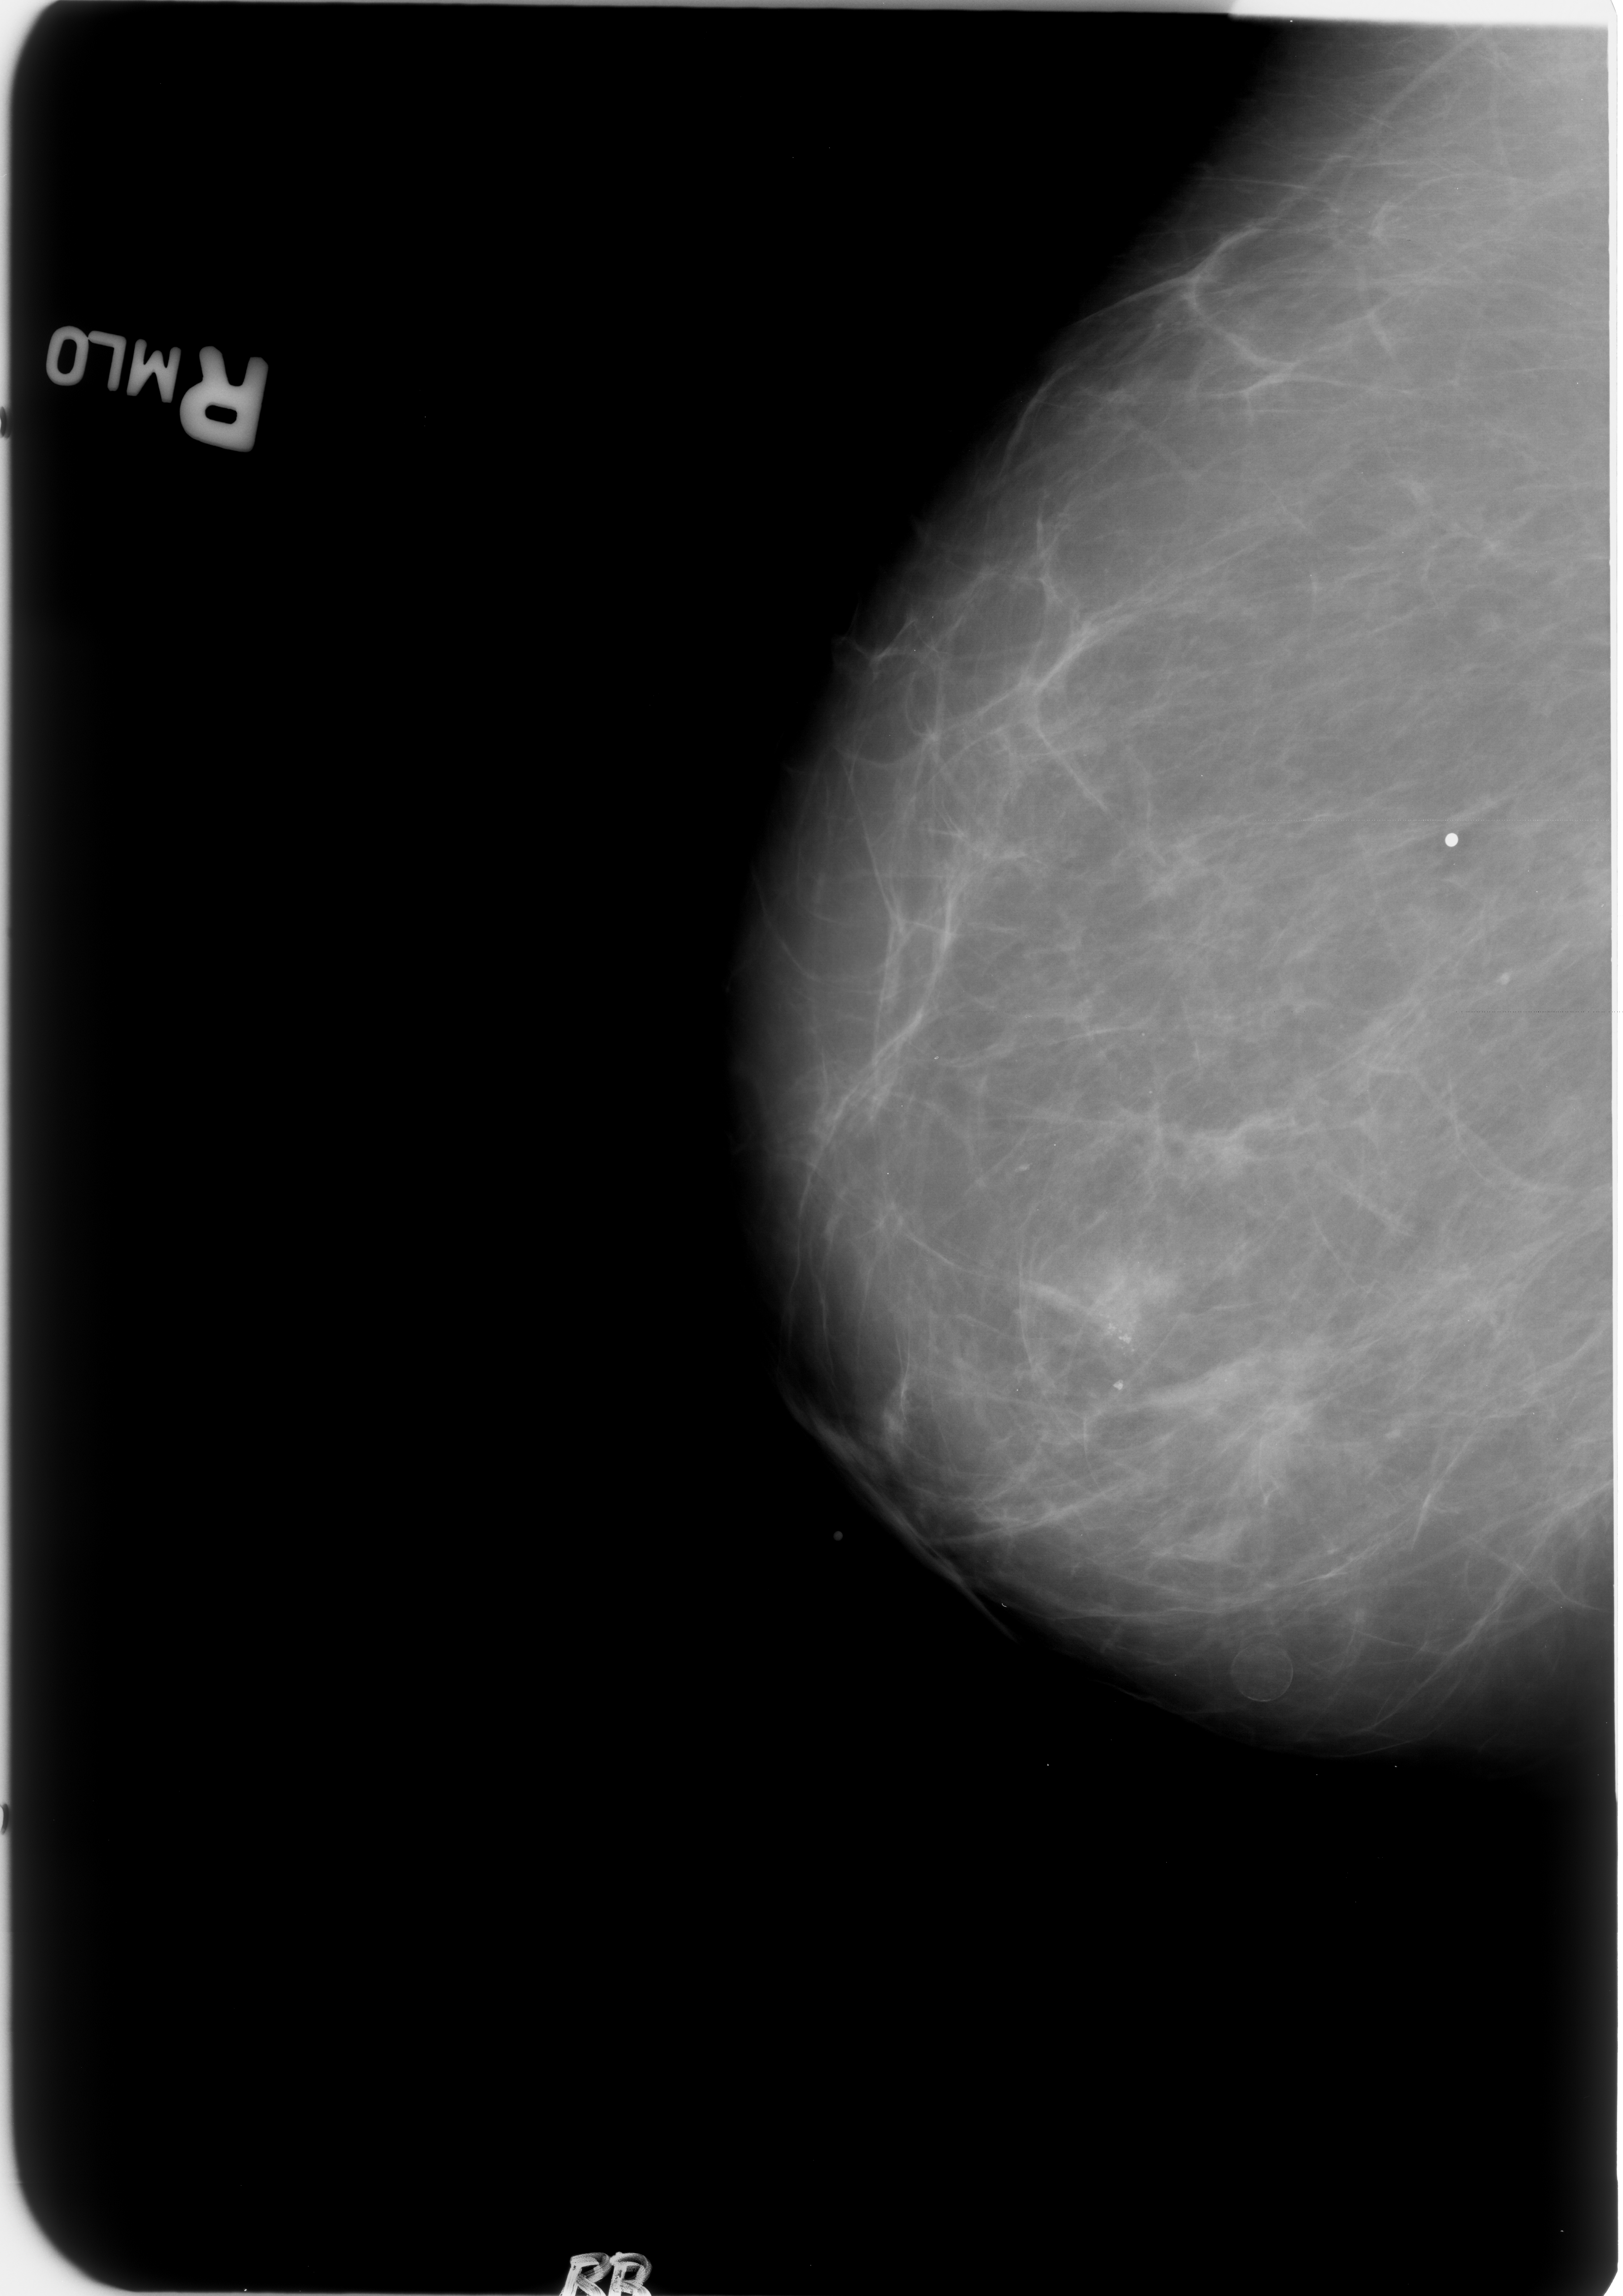
Scanned film-screen mammogram; right breast; MLO view; 1623 × 2296 image matrix.
Expert-marked regions of interest on this film, with their recorded descriptors:
- calcifications, morphology pleomorphic, distribution clustered; BI-RADS assessment category 4; subtlety rating 4 on a 1 (subtle) to 5 (obvious) scale; pathology result (as recorded, not read from the image): benign: bounding box <1084,1256,1184,1353> (left, top, right, bottom; pixels)